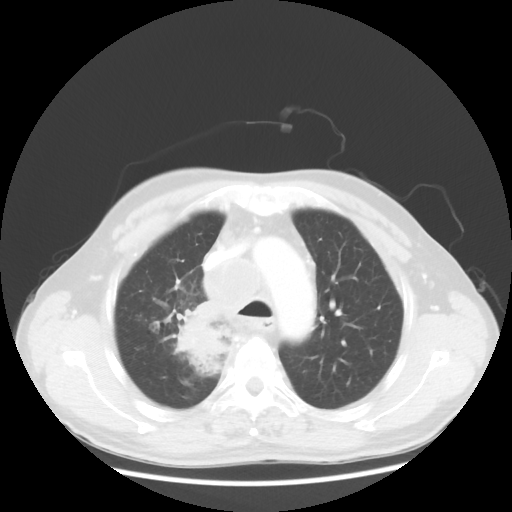
Chest CT, one axial slice; position 91 of 124 along the scan axis; lung window (W 1500 / L -600 HU); 5 mm slice thickness; 512 × 512 image matrix, field of view 382 × 382 mm. Patient: male, 64 years. Case-level facts recorded for this patient, not image findings: clinical TNM (as recorded): T3 N3 M0.
Annotated regions visible in this slice (bounding box drawn by a radiologist):
- lung tumour (recorded histology: small cell carcinoma): box from (x=172, y=306) to (x=233, y=377) px